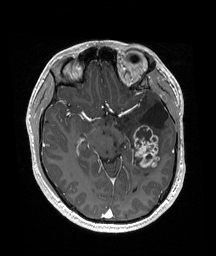
Brain MRI from a brain-tumour surgery series, one axial slice; slice 103 of 192 in the series (ordered by position); T1-weighted post-contrast; 1 mm slice thickness; 216 × 256 image matrix, field of view 211 × 250 mm. From the clinical record (not read from this slice): histopathology: Glioneuronal tumor; WHO grade: 2.
Structures marked on this image (expert manual segmentation):
- previous resection cavity: bounding box (x1, y1, x2, y2) in pixels: (140, 103, 169, 128)
- tumour: (131, 125, 160, 167)